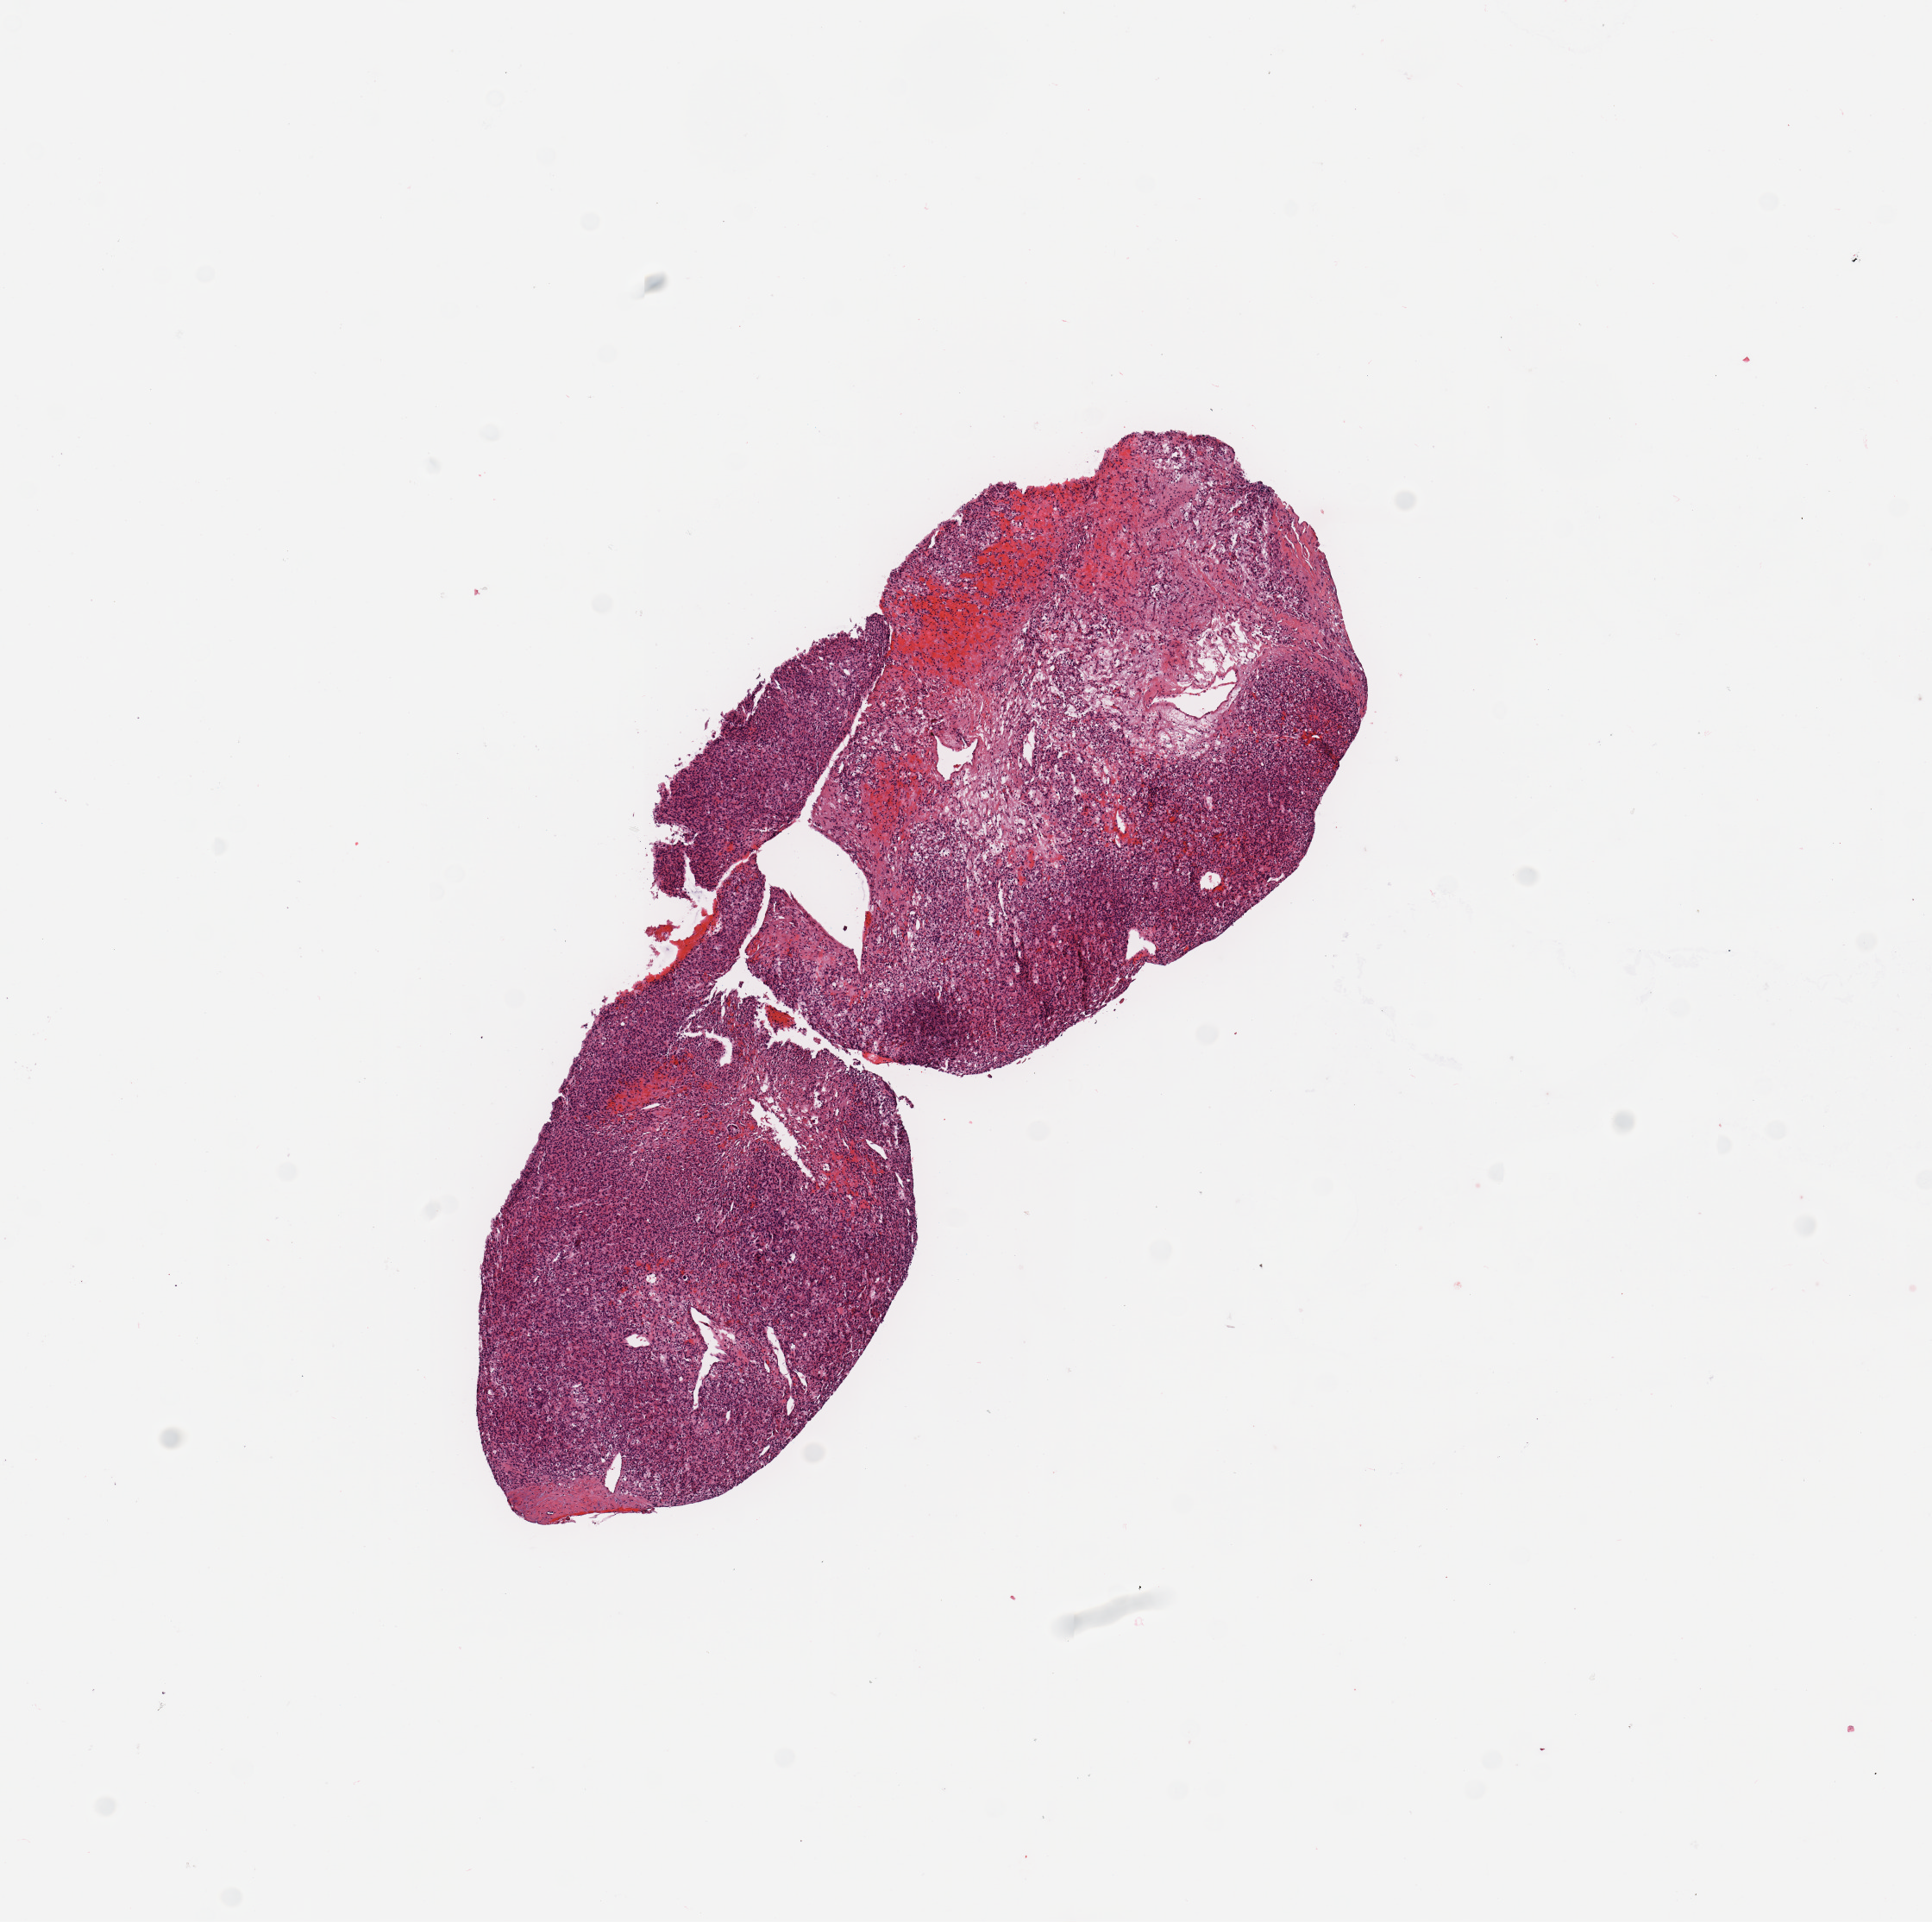
Whole-slide histology image, H&E — low-resolution overview of the scanned area, about 8.9 x 8.8 mm (from a 20x scan); tumour tissue sample, sampled site: kidney. 57-year-old female patient. Histologic grade: G2 (moderately differentiated). Pathologist review of this section (percent, as recorded): tumour nuclei 80%, necrosis 0%.
AJCC pathologic stage: I. Primary tumour site (as recorded): lower pole. Diagnosis: Renal cell carcinoma, NOS.